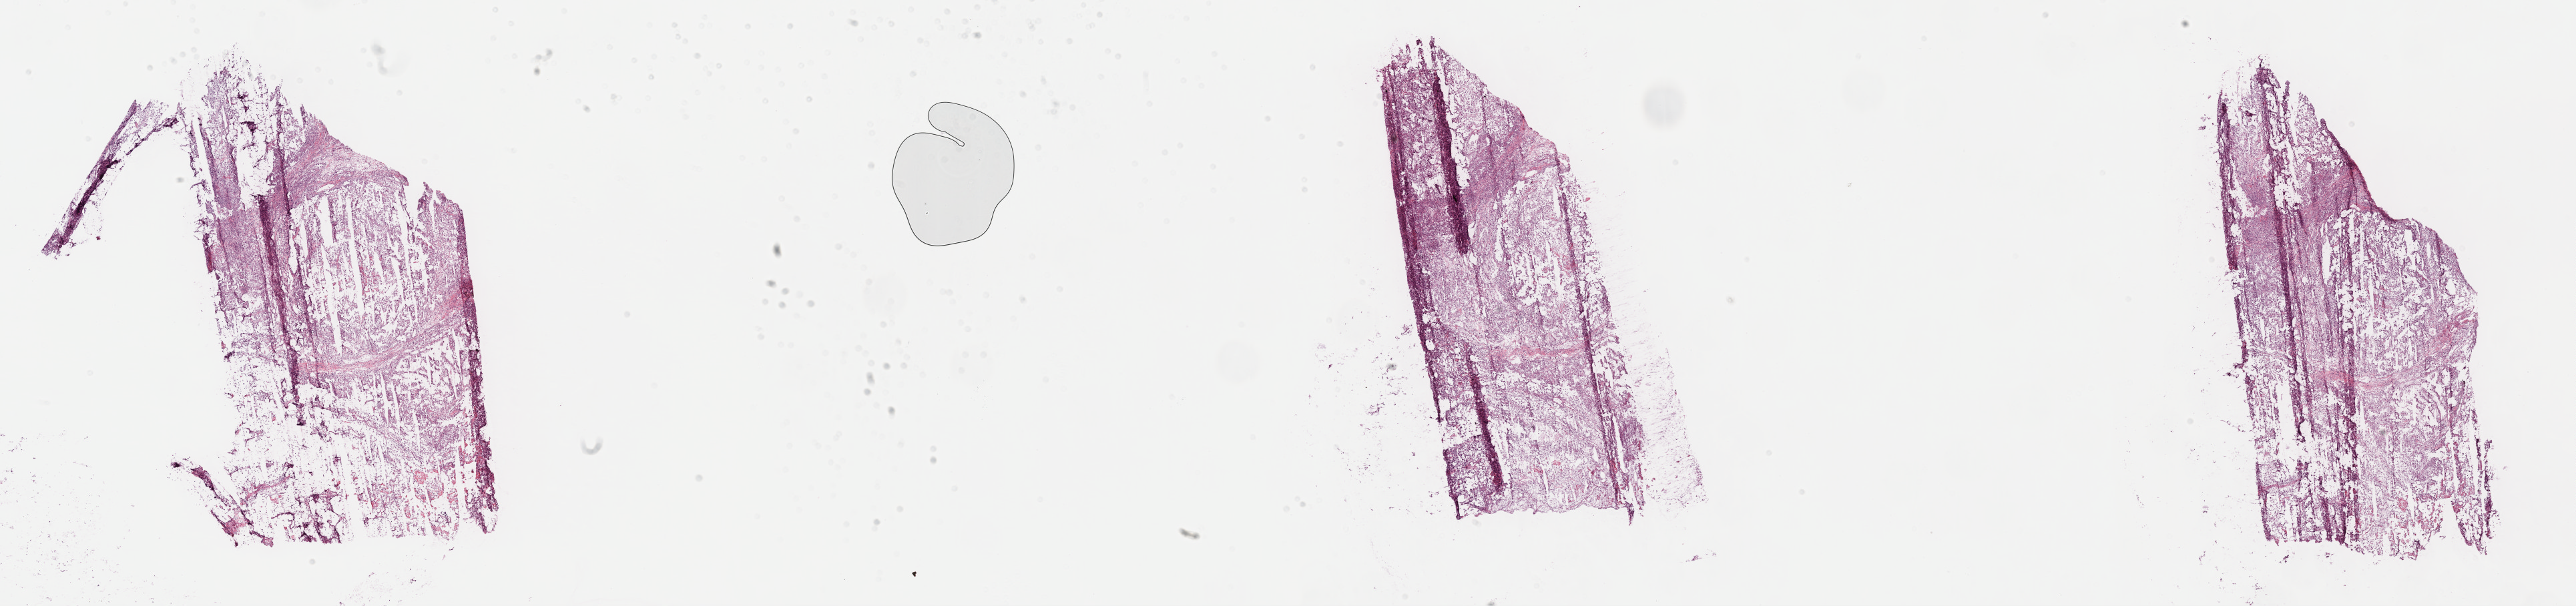
Whole-slide histology image, H&E, a low-resolution overview of the entire scanned area, about 31.2 x 7.3 mm (acquisition: 40x scan), frozen section, kidney, primary tumour sample. Male patient; age at initial diagnosis 79 years. Histologic grade: G3 (poorly differentiated). Pathologist review of this section (percent, as recorded): tumour cells 95%, tumour nuclei 85%, normal cells 0%, stromal cells 5%, necrosis 0%.
* AJCC pathologic stage: I
* histologic diagnosis: Clear cell adenocarcinoma, NOS